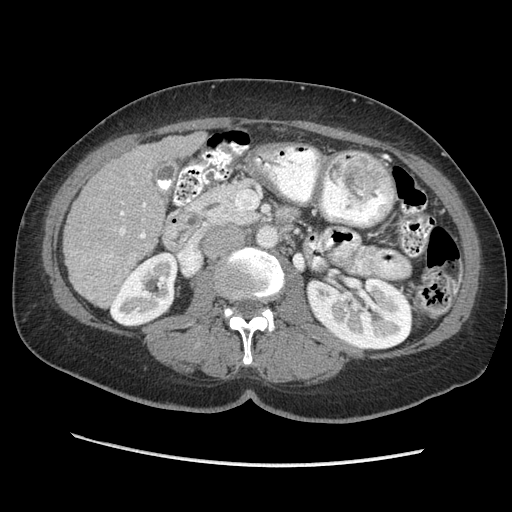
Contrast-enhanced abdominal CT (liver protocol), one axial slice. Reconstruction kernel STANDARD. 140 kVp. Soft-tissue window (W 400 / L 40 HU). 512 × 512 image matrix. From the clinical record (not read from this slice): diagnosis: hepatocellular carcinoma (patient treated with transarterial chemoembolisation; whether this scan precedes or follows treatment is not stated here); TNM stage (as recorded): Stage-II.
Outlined on this slice (semi-automatic segmentation, software-assisted and operator-edited):
- liver parenchyma outside the tumour (the mass and vessels are separate outlines, so this box may not span the whole liver): bounding box <64,132,206,306> (left, top, right, bottom; pixels)
- liver vessels: <103,203,146,259>